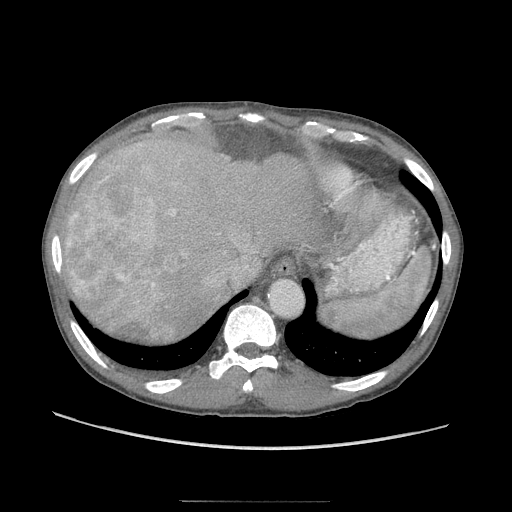
Contrast-enhanced abdominal CT (liver protocol), one axial slice. Position 79 of 103 along the scan axis. Reconstruction kernel STANDARD. 120 kVp. Soft-tissue window (W 400 / L 40 HU). 2.5 mm slice thickness. 512 × 512 image matrix. From the clinical record (not read from this slice): diagnosis: hepatocellular carcinoma (patient treated with transarterial chemoembolisation; whether this scan precedes or follows treatment is not stated here); TNM stage (as recorded): Stage-IIIA; Child-Pugh class: A; tumour size: 16 cm.
Annotated regions visible in this slice (semi-automatic segmentation, software-assisted and operator-edited):
- abdominal aorta: bounding box <269,280,302,316> (left, top, right, bottom; pixels)
- liver parenchyma outside the tumour (the mass and vessels are separate outlines, so this box may not span the whole liver): <64,116,306,343>
- mass: <64,179,188,336>
- liver vessels: <140,117,207,286>